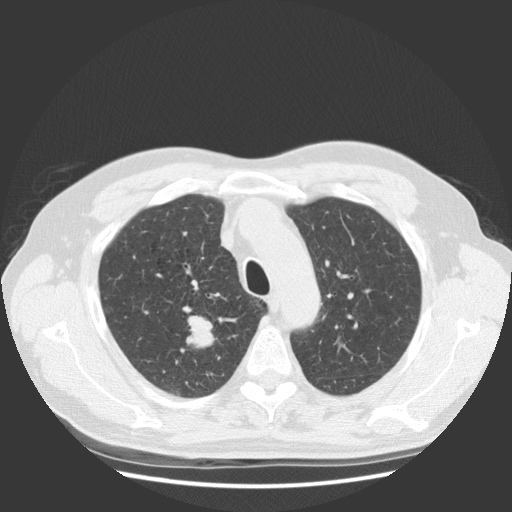
Low-dose screening chest CT, axial slice, baseline annual screen, lung window (W 1500 / L -600 HU), 140 kVp, 512 × 512 image matrix. Male, age 63 years at enrolment.
Expert reader's lesion annotation, bounding box <157,303,229,377> (left, top, right, bottom; pixels). The screening reader recorded 2 non-calcified nodules or masses ≥4 mm on this exam; which of them this box marks is not recorded. Participant outcome: lung cancer diagnosed 30 days after this screen — squamous cell carcinoma, NOS, right upper lobe, stage IIIB (AJCC 6th edition), 35 mm at pathology.